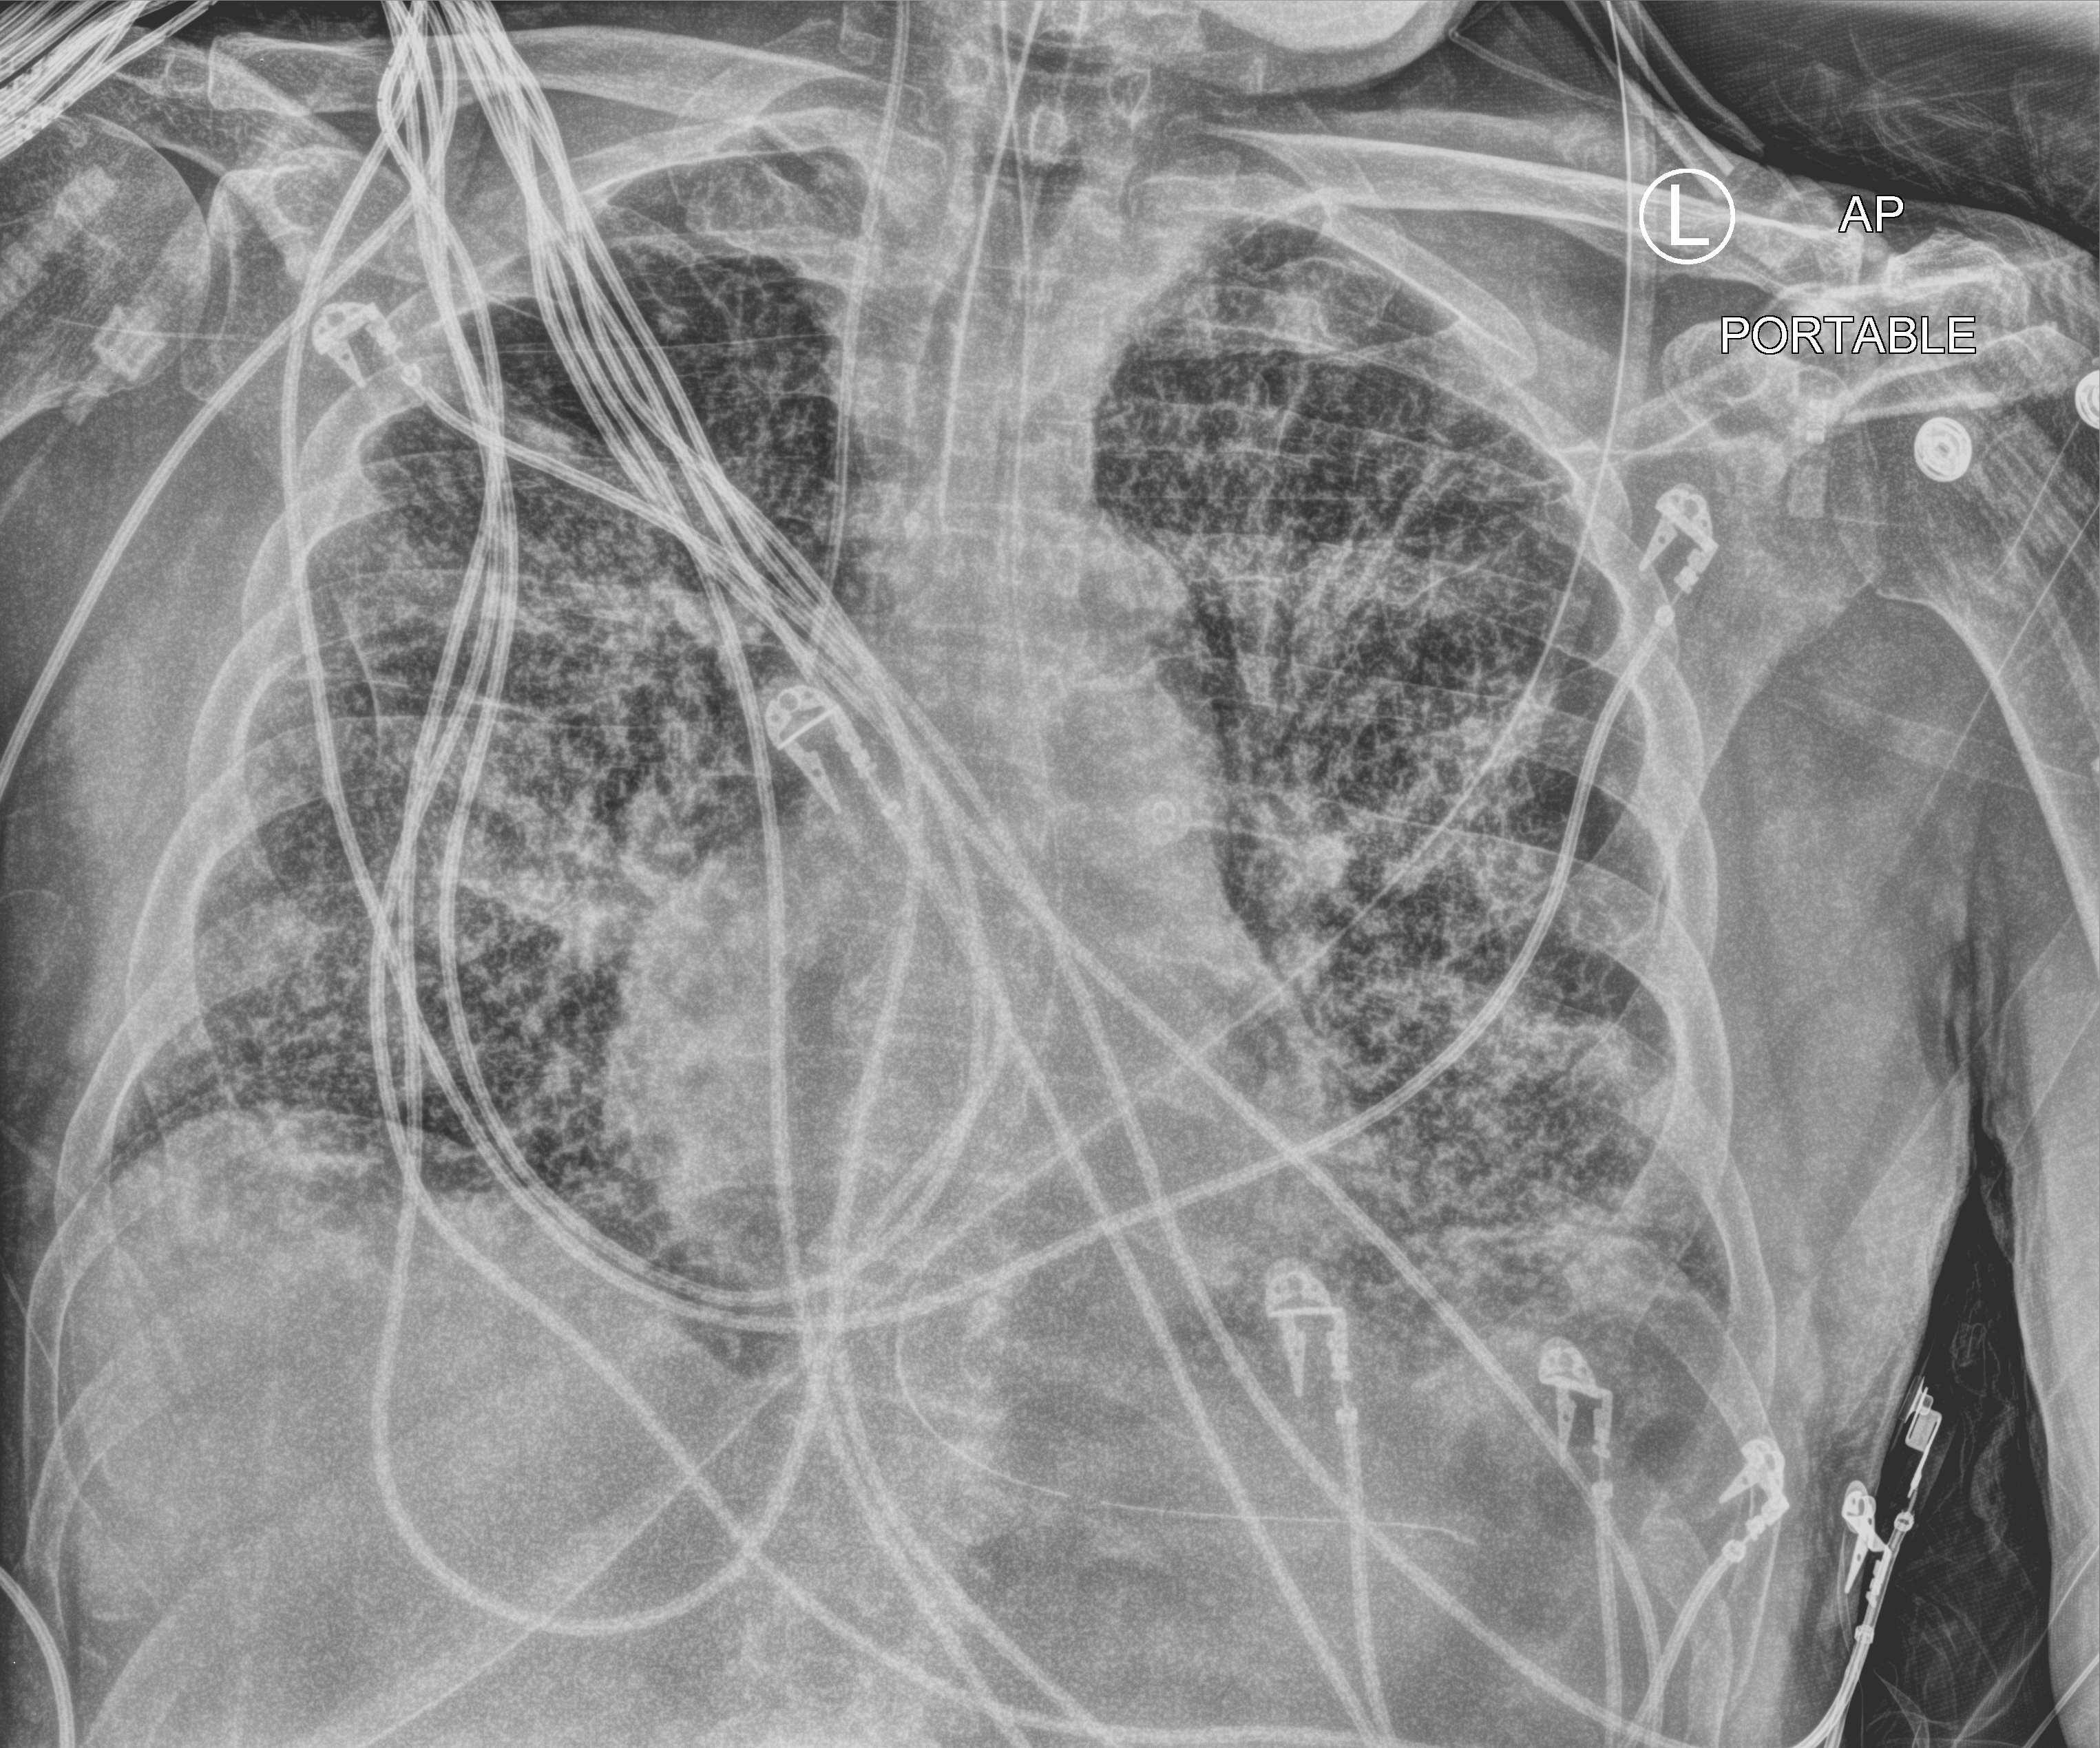
Portable chest radiograph, anteroposterior (AP) projection. Patient hospitalised with COVID-19; male, aged 75–90 years.
Admission-level facts for this patient (not findings on this image; timing relative to this image not recorded):
- admitted to intensive care during this hospital stay: yes
- other chronic lung disease (admission record): yes
- chronic kidney disease (admission record): no